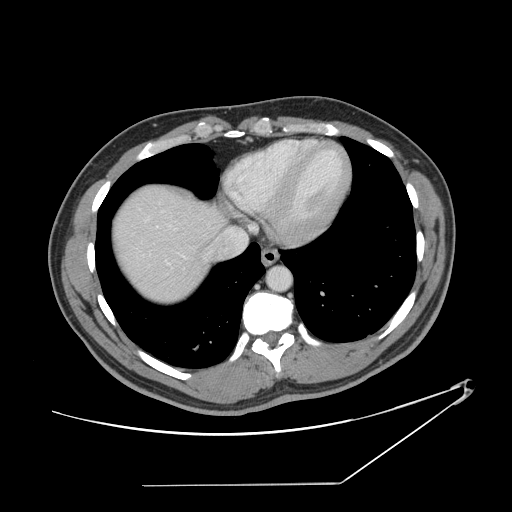
Contrast-enhanced abdominal CT, one axial slice. Position 133 of 152 along the scan axis. Intravenous contrast given. Soft-tissue window (W 400 / L 40 HU). 2.5 mm slice thickness. 512 × 512 image matrix, field of view 432 × 432 mm. Male patient, age 45 years. From the clinical record (not read from this slice): diagnosis: colorectal cancer liver metastases, imaged before liver resection; multiple liver metastases: no; largest metastasis: 1 cm; disease in both lobes: no.
Structures marked on this image (expert manual segmentation):
- hepatic veins: bounding box <156,211,247,248> (left, top, right, bottom; pixels)
- liver: <115,187,222,304>
- planned liver remnant (the part of the liver to remain after resection): <115,187,222,303>